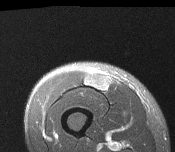
MRI of an extremity soft-tissue mass, one axial slice. Position 38 of 116 along the scan axis. T2-weighted fat-saturated. MR volume resampled by the dataset authors to the PET/CT grid (not the native acquisition matrix). 3.27 mm slice thickness. 175 × 152 image matrix, field of view 171 × 148 mm. Male patient. Case-level facts recorded for this patient, not image findings: histological type: pleiomorphic leiomyosarcoma; grade: intermediate; site of the primary tumour: right thigh.
Annotated regions visible in this slice (expert contour drawn on MRI and transferred to this co-registered scan by the dataset authors):
- gross tumour volume including surrounding oedema: box from (x=85, y=74) to (x=109, y=91) px